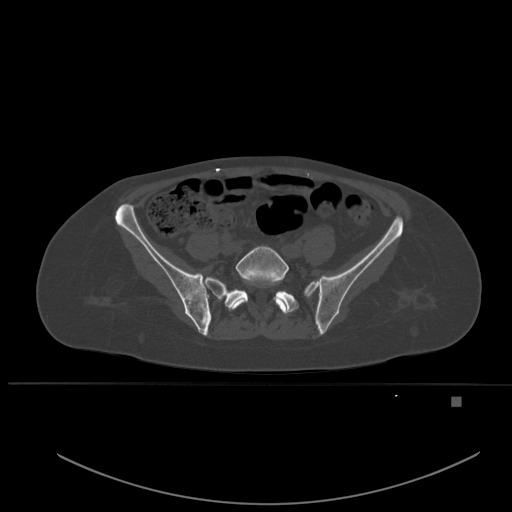
CT including the spine, one axial slice. Slice 146 of 651 in the series (ordered by position). Bone window (W 1800 / L 400 HU). 512 × 512 image matrix, field of view 443 × 443 mm. Female patient, age 49 years. Case-level facts recorded for this patient, not image findings: primary cancer: breast; vertebrae with lytic lesions (as recorded): L3, T12, L4.
Structures marked on this image (semi-automatic segmentation, software-assisted and operator-edited):
- L5 vertebra: bounding box <230,246,289,314> (left, top, right, bottom; pixels)